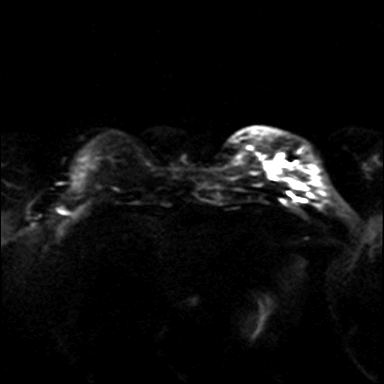
Breast MRI, one axial slice. Position 5 of 36 along the scan axis. Diffusion-weighted series; image 2 of 4 stored at this slice position (different b-values; order by instance number). 3 T. 4 mm slice thickness. 384 × 384 image matrix, field of view 320 × 320 mm. Female patient.
Annotated regions visible in this slice (expert manual segmentation):
- tumour on diffusion-weighted imaging: bounding box <269,155,281,177> (left, top, right, bottom; pixels)